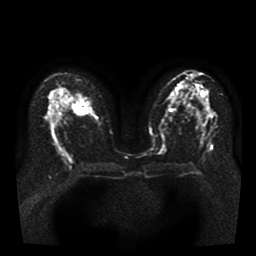
Breast MRI, one axial slice. Position 22 of 41 along the scan axis. Diffusion-weighted series; image 2 of 4 stored at this slice position (different b-values; order by instance number). 1.5 T. 5 mm slice thickness. 256 × 256 image matrix, field of view 330 × 330 mm. Female patient.
Annotated regions visible in this slice (manually delineated by an expert):
- tumour on diffusion-weighted imaging: bounding box [x1, y1, x2, y2] px = [69, 102, 87, 115]